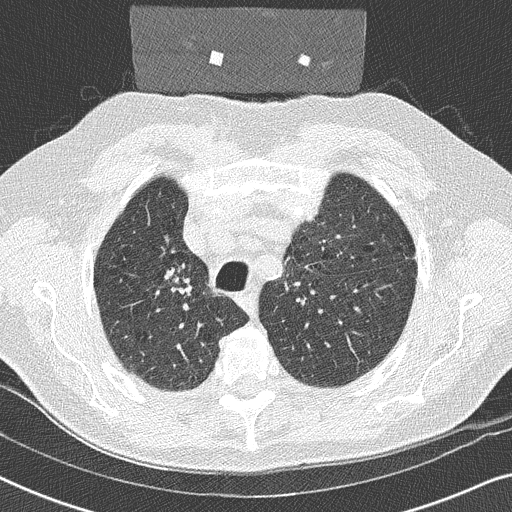
Low-dose screening chest CT, one axial slice; position 187 of 252 along the scan axis; reconstruction kernel B50f; 120 kVp; lung window (W 1500 / L -600 HU); 2 mm slice thickness; 512 × 512 image matrix, field of view 330 × 330 mm.
Annotated regions visible in this slice (manually delineated by an expert):
- lesion 1 (tumor, upper lobe of right lung): bounding box <173,275,181,284> (left, top, right, bottom; pixels)